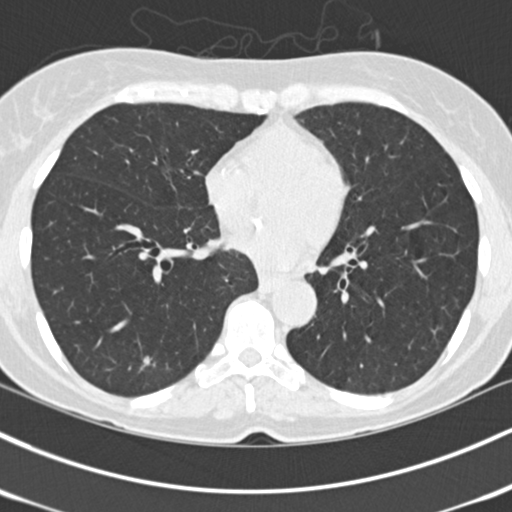
Low-dose screening chest CT, one axial slice. Position 60 of 150 along the scan axis. 120 kVp. Lung window (W 1500 / L -600 HU). 512 × 512 image matrix, field of view 318 × 318 mm.
Structures marked on this image (manually delineated by an expert):
- lesion 1 (tumor): box from (x=143, y=356) to (x=150, y=367) px